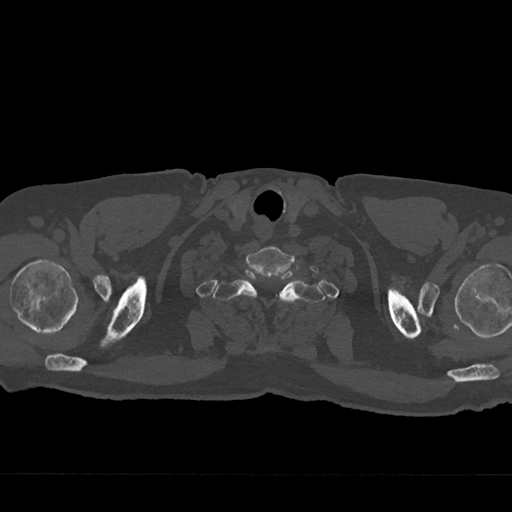
CT including the spine, one axial slice; position 672 of 797 along the scan axis; 120 kVp; bone window (W 1800 / L 400 HU); 0.5 mm slice thickness; 512 × 512 image matrix, field of view 377 × 377 mm. Patient: male, 75 years. Case-level facts recorded for this patient, not image findings: primary cancer: renal; vertebrae with lytic lesions (as recorded): T4.
Annotated regions visible in this slice (semi-automatically segmented with operator editing):
- T1 vertebra: bounding box [x1, y1, x2, y2] px = [213, 270, 324, 303]